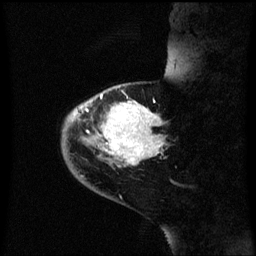
Breast MRI (dynamic contrast-enhanced), one sagittal slice. Position 15 of 60 along the scan axis. Dynamic contrast-enhanced series, image 2 of 3 at this slice position (ordered by acquisition). 1.5 T. TE 4.2 ms, TR 8.4 ms. 2.3 mm slice thickness. 256 × 256 image matrix. Patient: female, 46 years. Case-level facts recorded for this patient, not image findings: setting: breast cancer imaged before/during neoadjuvant chemotherapy; receptor status: HER2-positive.
Annotated regions visible in this slice (semi-automatically segmented with operator editing):
- analysis volume of interest (the breast-tissue region the enhancement analysis was run in; not a lesion): box from (x=62, y=86) to (x=167, y=171) px
- tumour enhancement mask (voxels above the 70 % enhancement threshold inside the analysis volume of interest): (x=72, y=94)–(x=163, y=167)